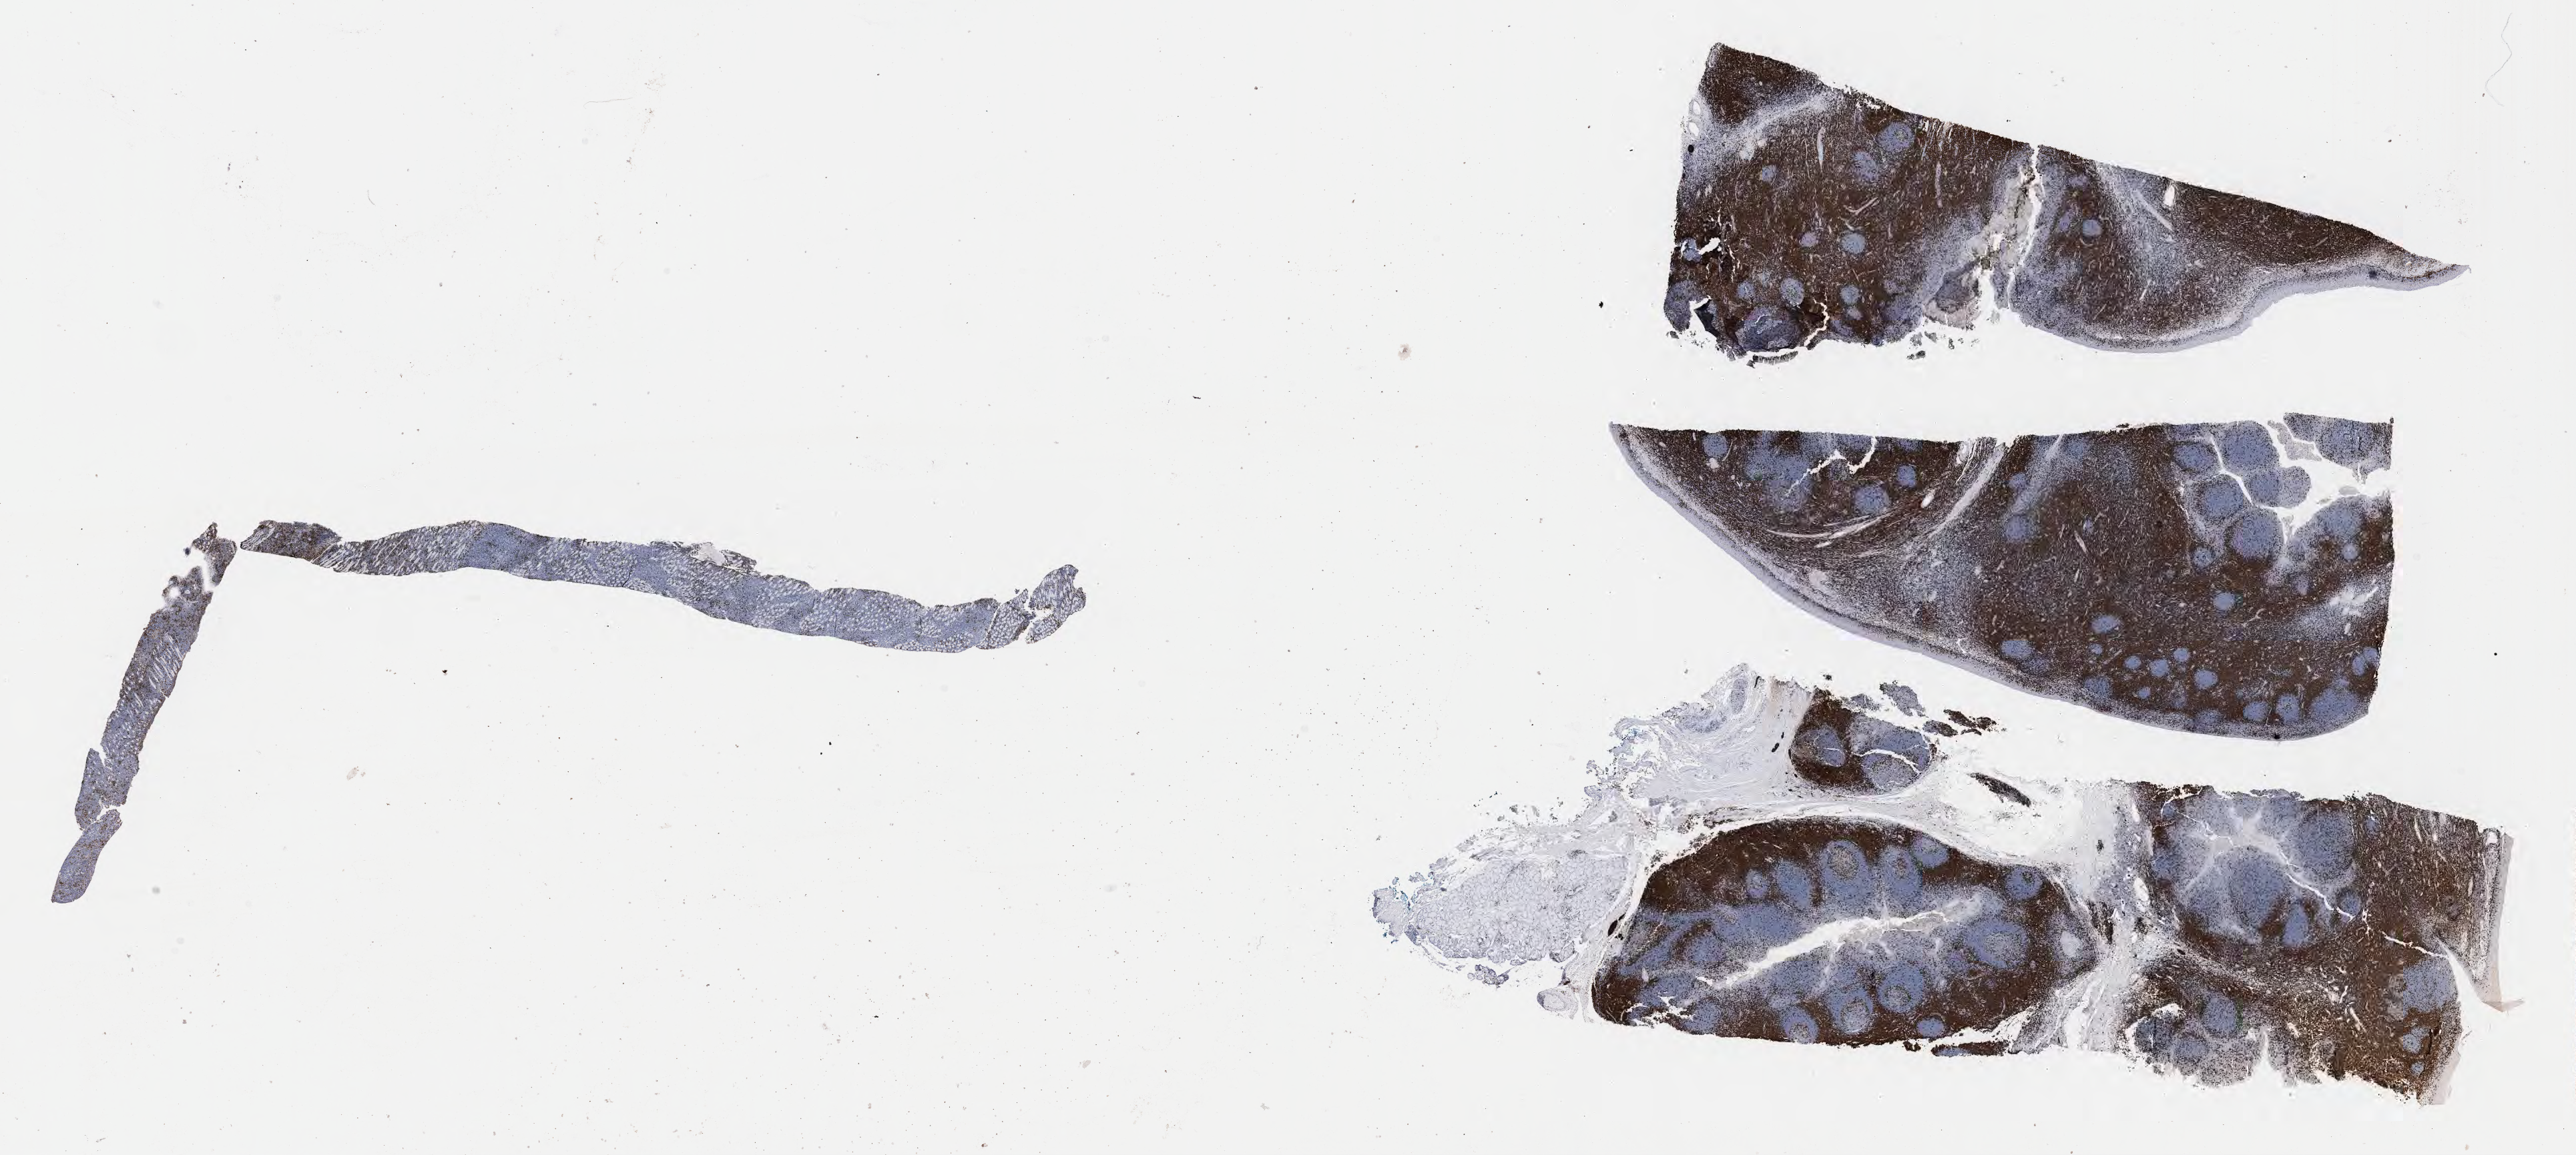
Whole-slide image, immunohistochemical stain for CD3 — shown as a low-resolution overview of the whole scanned area (about 31.2 x 14.0 mm). Specimen: tumor tissue. Male patient; age at initial diagnosis 4 years.
• diagnosis: Burkitt lymphoma, NOS